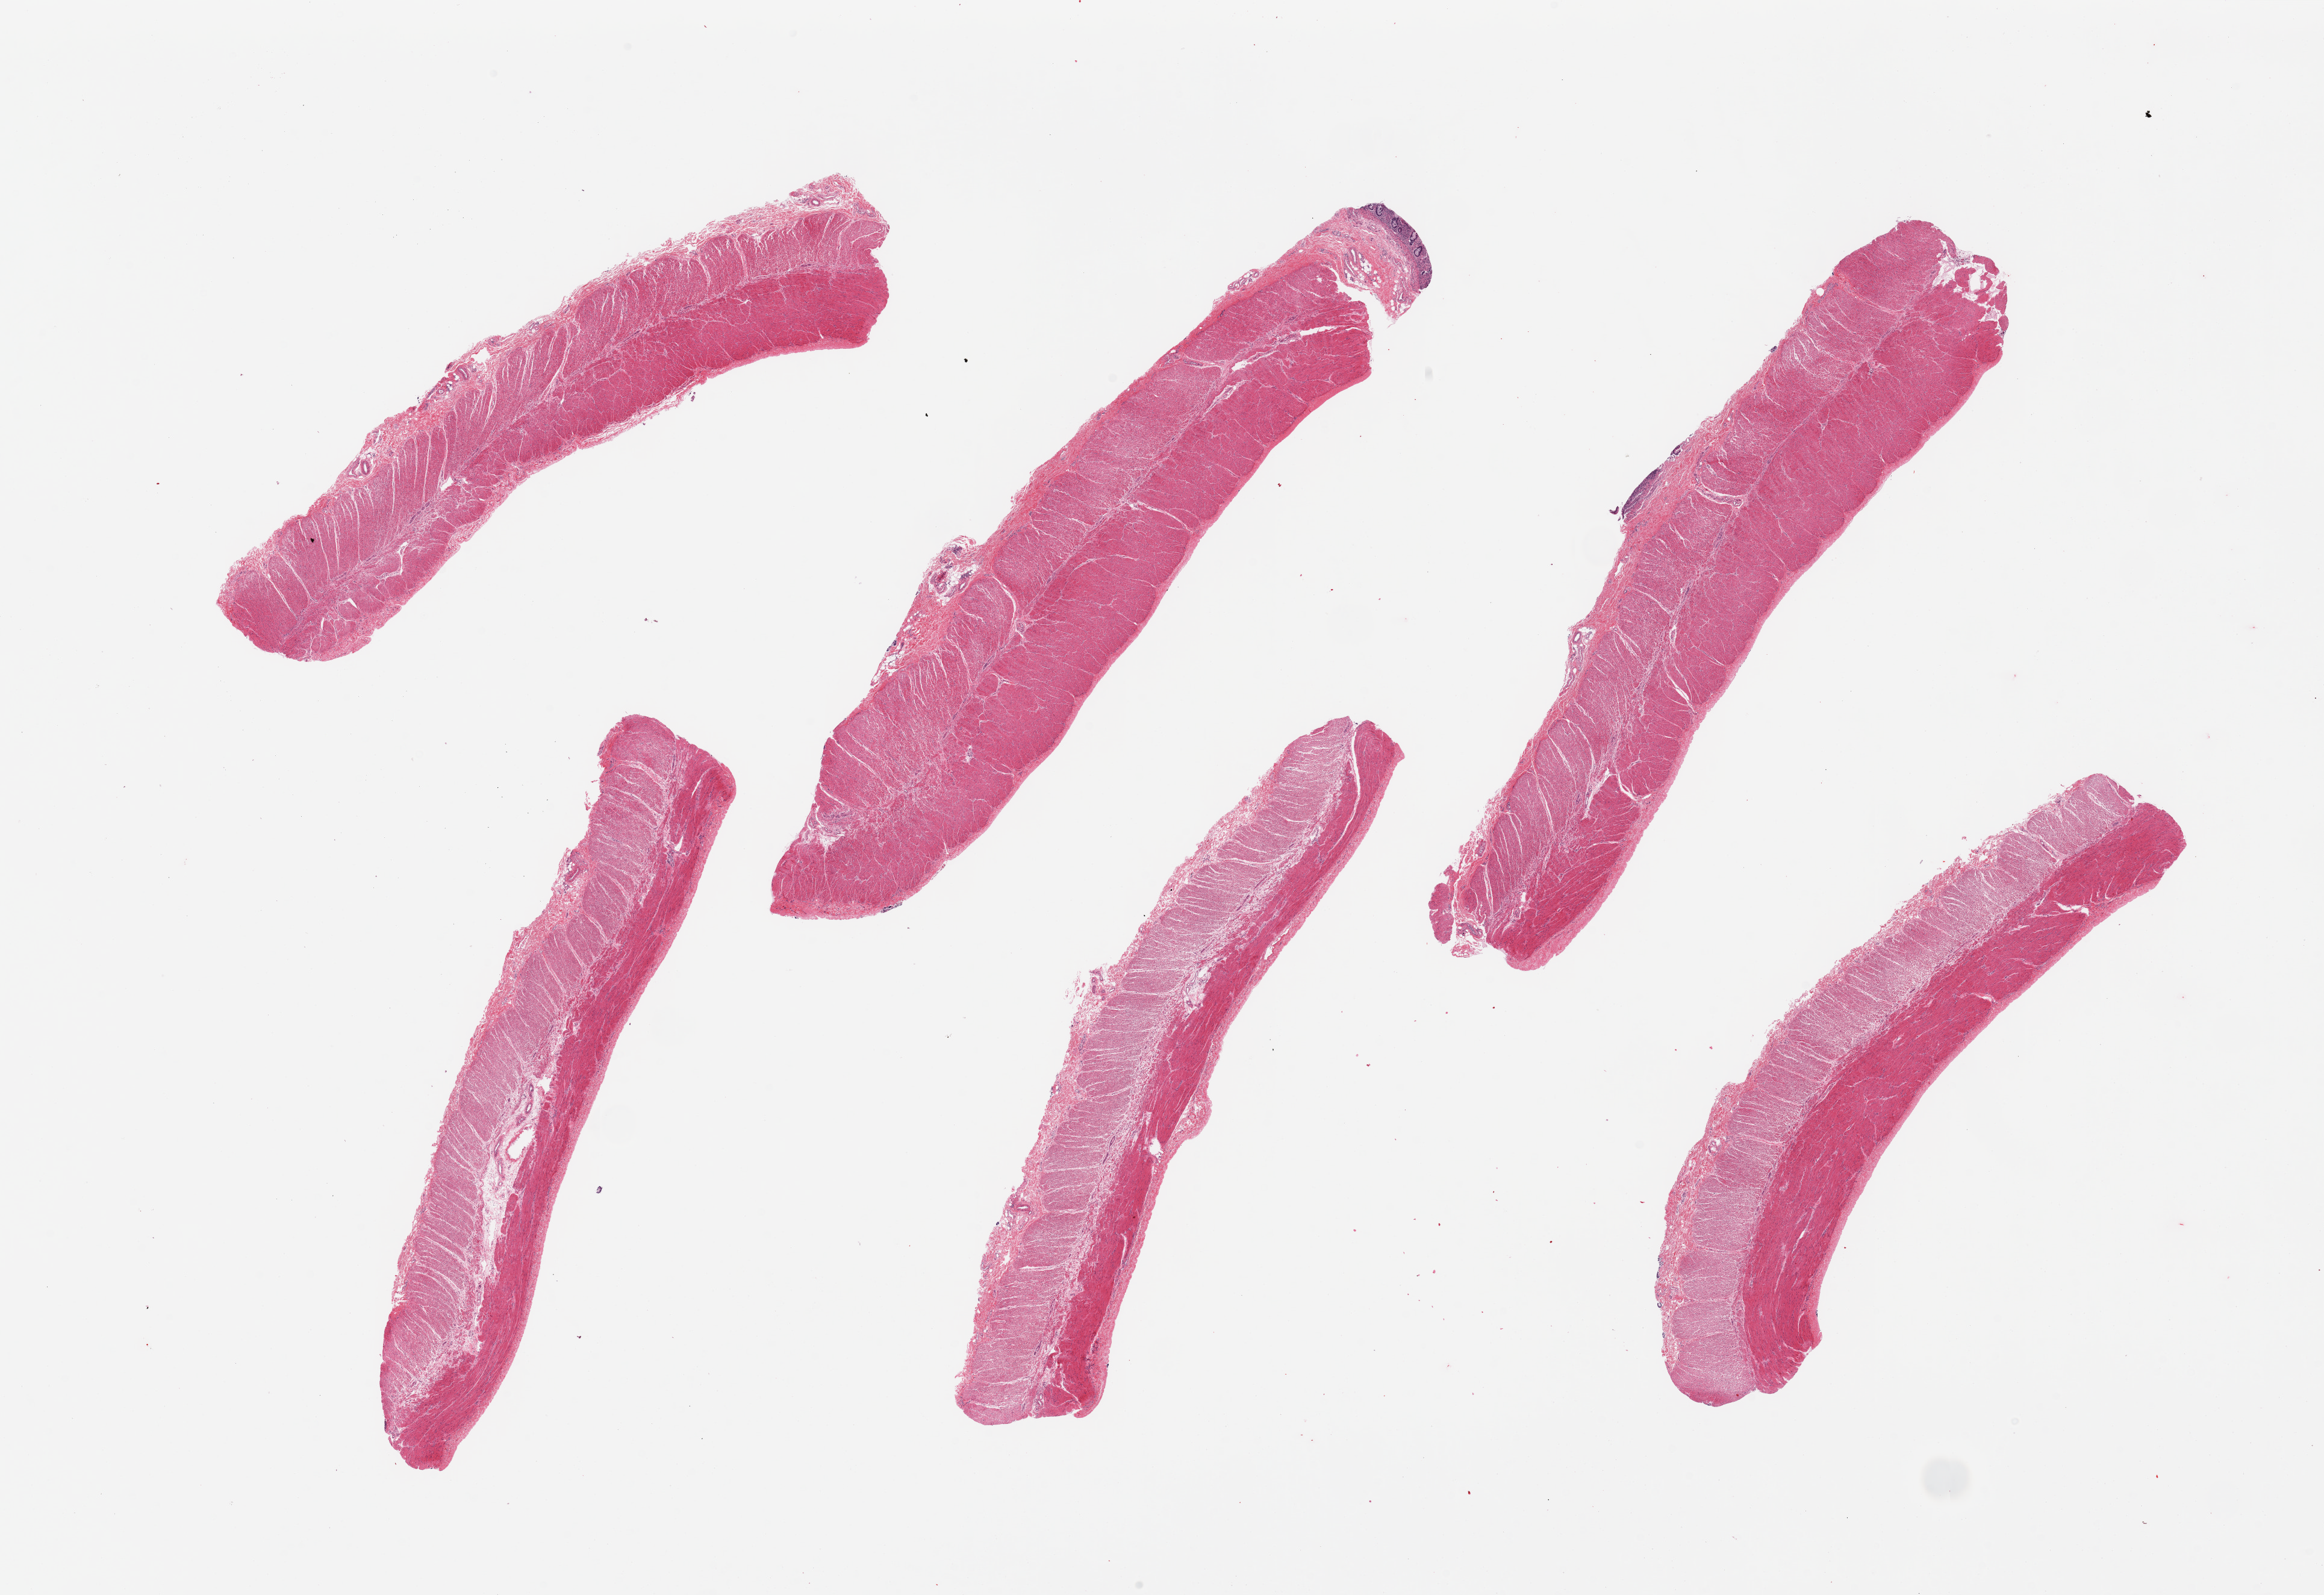
Digitized hematoxylin and eosin (H&E)-stained section, brightfield, a low-resolution overview of the entire scanned area, about 30.5 x 20.9 mm (acquisition: 20x scan). PAXgene-fixed paraffin-embedded (PFPE) section. Section of sigmoid colon (target tissue). Donor tissue sample.
Review note (as recorded): 6 pieces, one piece contains small fragment of mucosa.